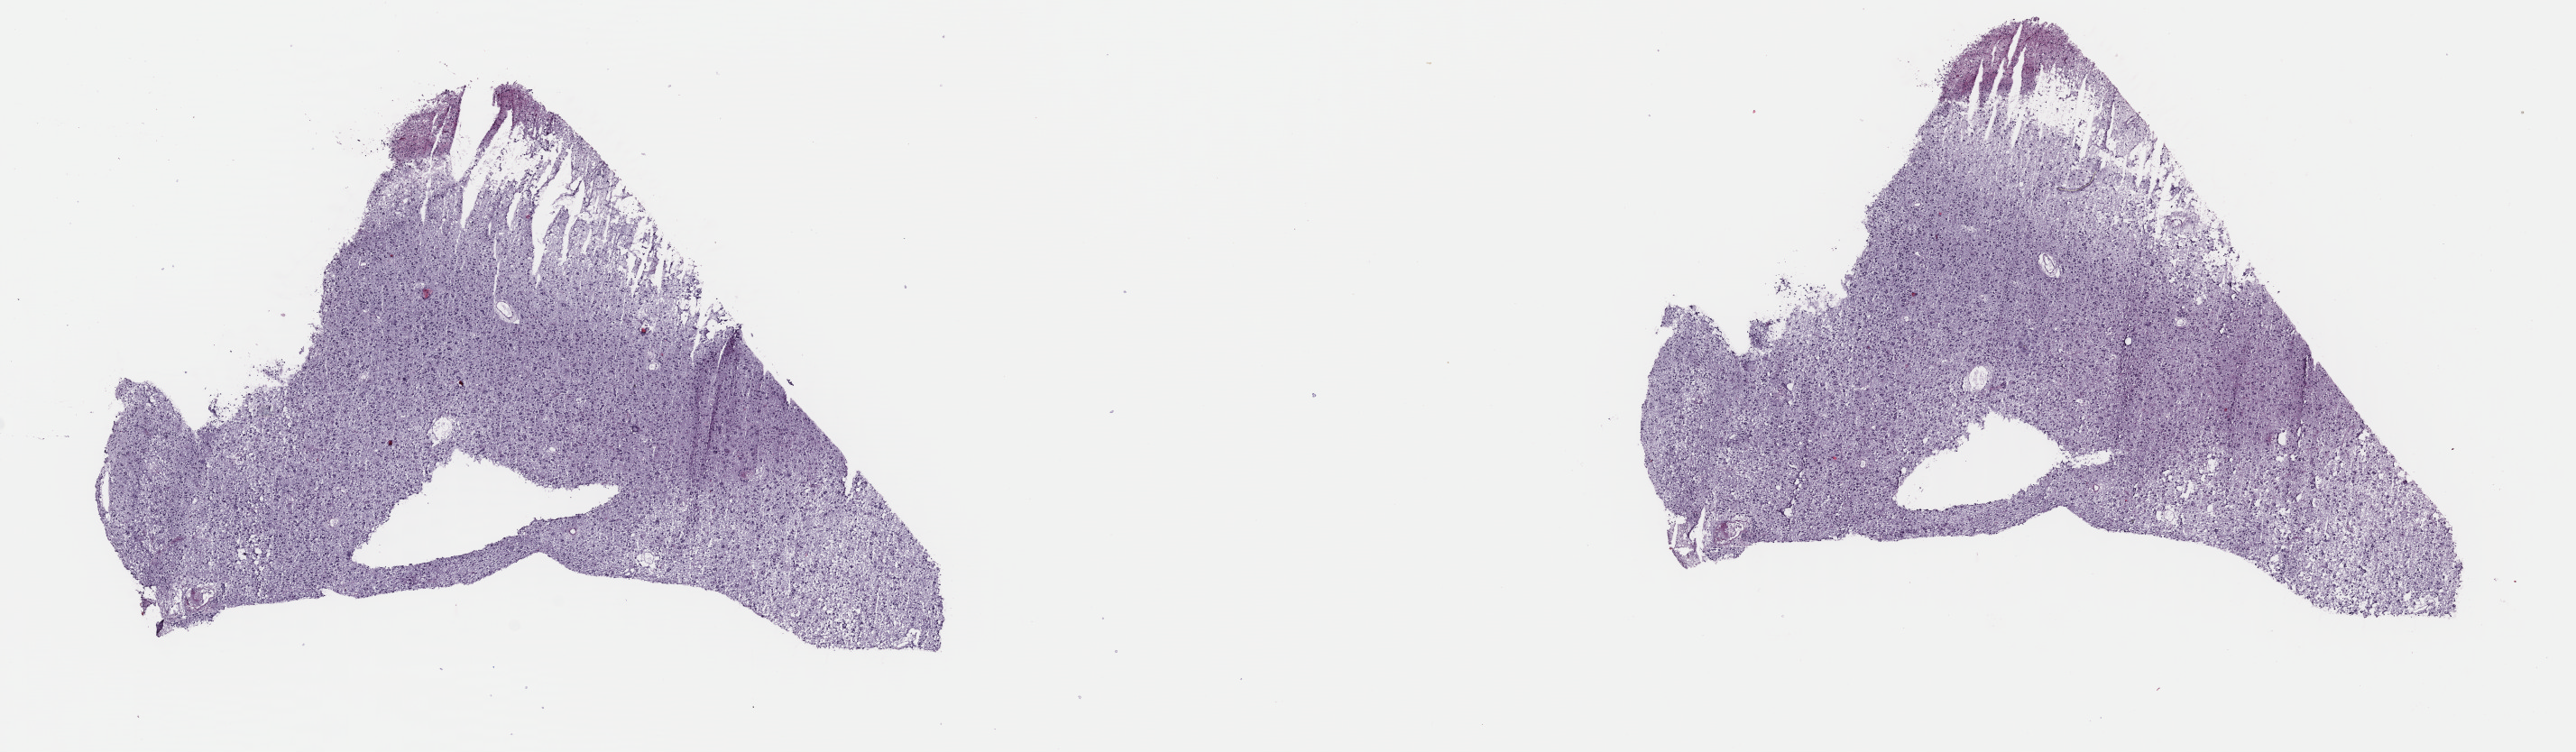
Whole-slide histology image, H&E-stained — low-resolution overview of the scanned area, about 22.5 x 6.6 mm (slide scanned at 40x). Frozen section from the top of the tissue portion. Sample: primary tumour, brain. Patient: female, age at initial diagnosis 67 years. Histologic grade: G2 (moderately differentiated). Pathologist review of this section (percent, as recorded): tumour cells 75%, tumour nuclei 80%, normal cells 5%, stromal cells 20%, necrosis 0%. Infiltration values recorded for this section: lymphocyte infiltration 0%, monocyte infiltration 0%, neutrophil infiltration 0%.
Histologic diagnosis: Oligodendroglioma, NOS (cerebrum).